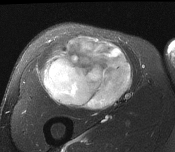
MRI of an extremity soft-tissue mass, one axial slice; position 94 of 116 along the scan axis; T2-weighted fat-saturated; MR volume resampled by the dataset authors to the PET/CT grid (not the native acquisition matrix); 175 × 152 image matrix, field of view 171 × 148 mm. Male patient. Case-level facts recorded for this patient, not image findings: histological type: pleiomorphic leiomyosarcoma; grade: intermediate; site of the primary tumour: right thigh.
Annotated regions visible in this slice (expert contour drawn on MRI and transferred to this co-registered scan by the dataset authors):
- gross tumour volume including surrounding oedema: bounding box (x1, y1, x2, y2) in pixels: (42, 36, 132, 110)
- gross tumour volume (mass): (44, 36, 132, 110)